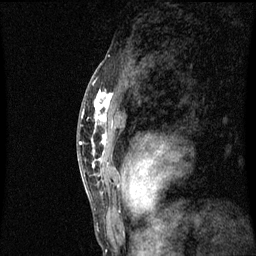
Breast MRI (dynamic contrast-enhanced), one sagittal slice; dynamic contrast-enhanced series, image 2 of 3 at this slice position (ordered by acquisition); 1.5 T; TE 4.2 ms, TR 8.9 ms; 2 mm slice thickness; 256 × 256 image matrix, field of view 200 × 200 mm. Female patient, age 50 years. Case-level facts recorded for this patient, not image findings: setting: breast cancer imaged before/during neoadjuvant chemotherapy; receptor status: triple-negative.
Outlined on this slice (semi-automatically segmented with operator editing):
- analysis volume of interest (the breast-tissue region the enhancement analysis was run in; not a lesion): bounding box <84,80,119,171> (left, top, right, bottom; pixels)
- tumour enhancement mask (voxels above the 70 % enhancement threshold inside the analysis volume of interest): <92,90,113,169>